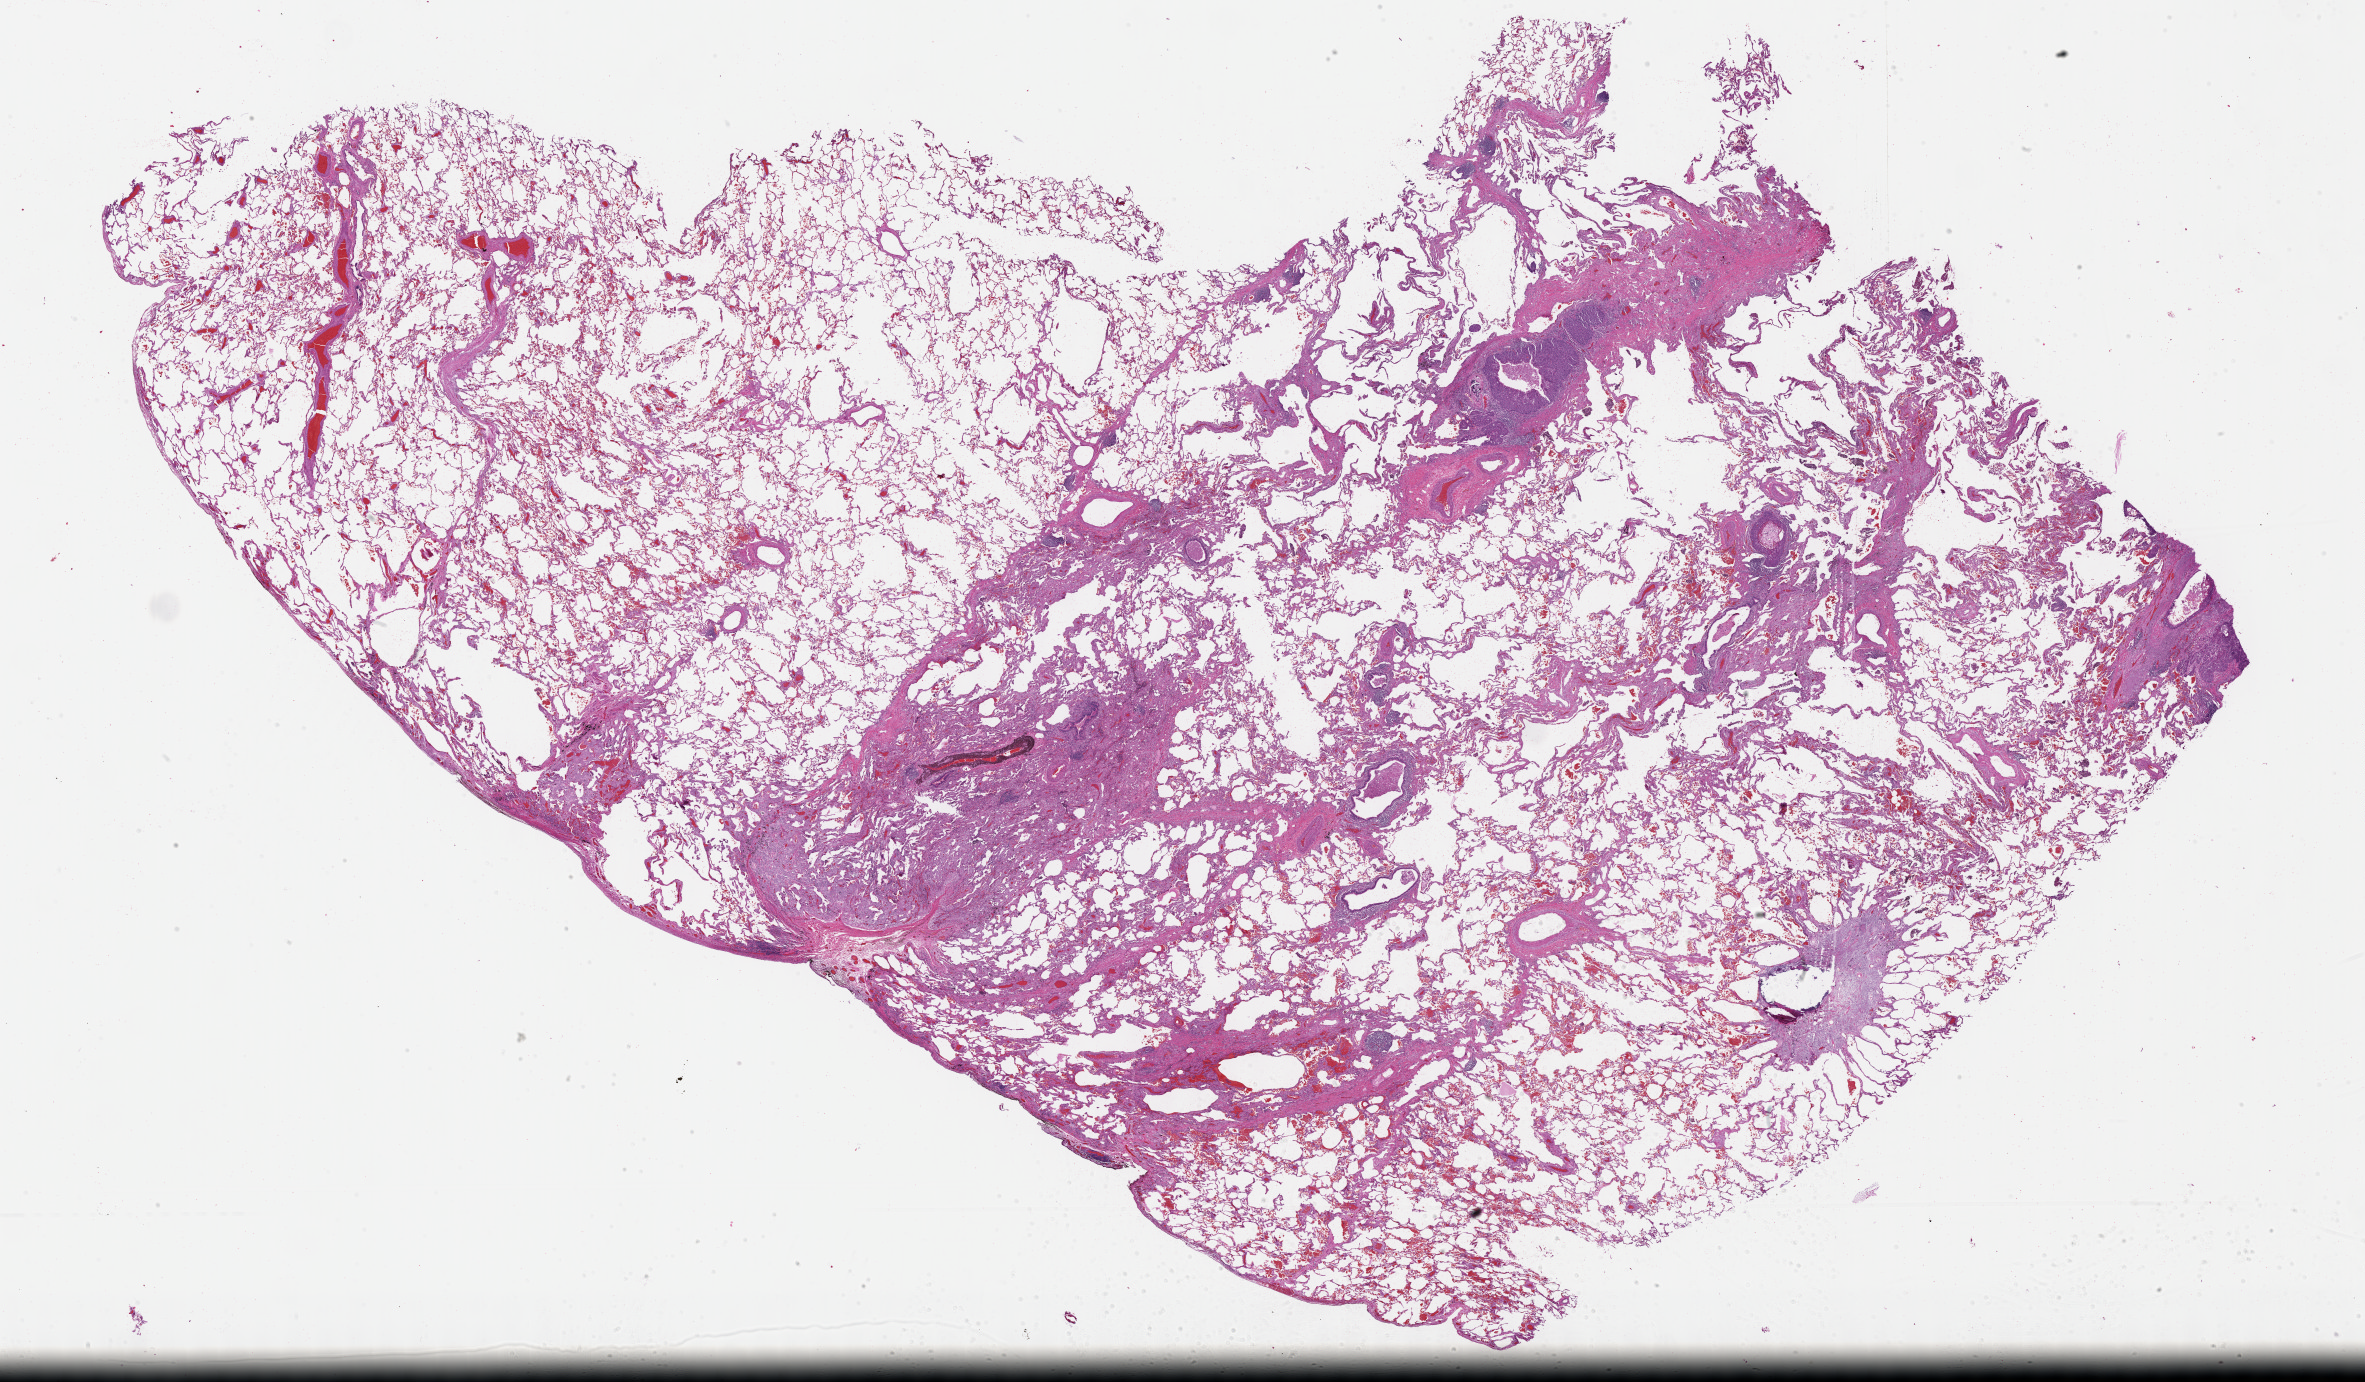
Whole-slide histology image, H&E — whole scanned area (about 38.3 x 22.4 mm) shown as a low-resolution overview, formalin-fixed paraffin-embedded (FFPE) diagnostic section, primary tumour sample from the lung. Male patient; age at initial diagnosis 60 years.
AJCC pathologic stage: IB. TNM: T2a N0 MX. Histologic diagnosis: Squamous cell carcinoma, NOS (upper lobe, lung).